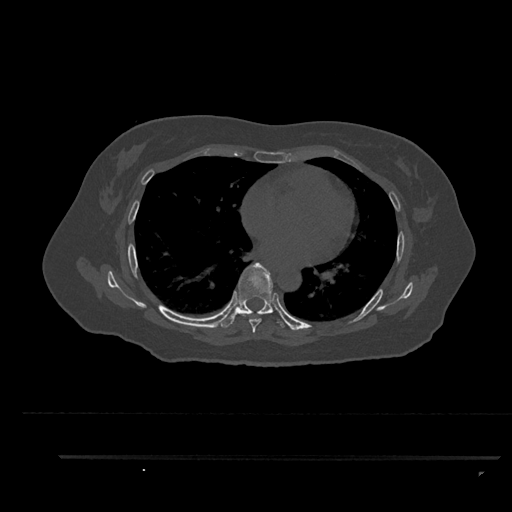
CT including the spine, one axial slice; position 530 of 797 along the scan axis; 120 kVp; bone window (W 1800 / L 400 HU); 0.5 mm slice thickness; 512 × 512 image matrix. Patient: female, 44 years. From the clinical record (not read from this slice): primary cancer: renal; vertebrae with lytic lesions (as recorded): L1.
Annotated regions visible in this slice (semi-automatic segmentation, software-assisted and operator-edited):
- T6 vertebra: bounding box [x1, y1, x2, y2] px = [242, 313, 267, 333]
- T7 vertebra: [220, 262, 286, 328]